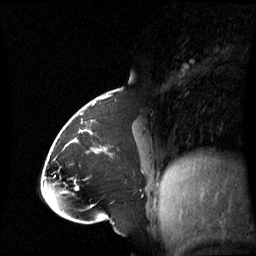
Breast MRI (dynamic contrast-enhanced), one sagittal slice; slice 27 of 60 in the series (ordered by position); dynamic contrast-enhanced series, image 2 of 3 at this slice position (ordered by acquisition); 1.5 T; TE 4.2 ms, TR 8.4 ms; 256 × 256 image matrix. Patient: female, 43 years. From the clinical record (not read from this slice): setting: breast cancer imaged before/during neoadjuvant chemotherapy; receptor status: triple-negative.
Annotated regions visible in this slice (semi-automatically segmented with operator editing):
- analysis volume of interest (the breast-tissue region the enhancement analysis was run in; not a lesion): bounding box (x1, y1, x2, y2) in pixels: (65, 118, 143, 198)
- tumour enhancement mask (voxels above the 70 % enhancement threshold inside the analysis volume of interest): (91, 120, 95, 134)